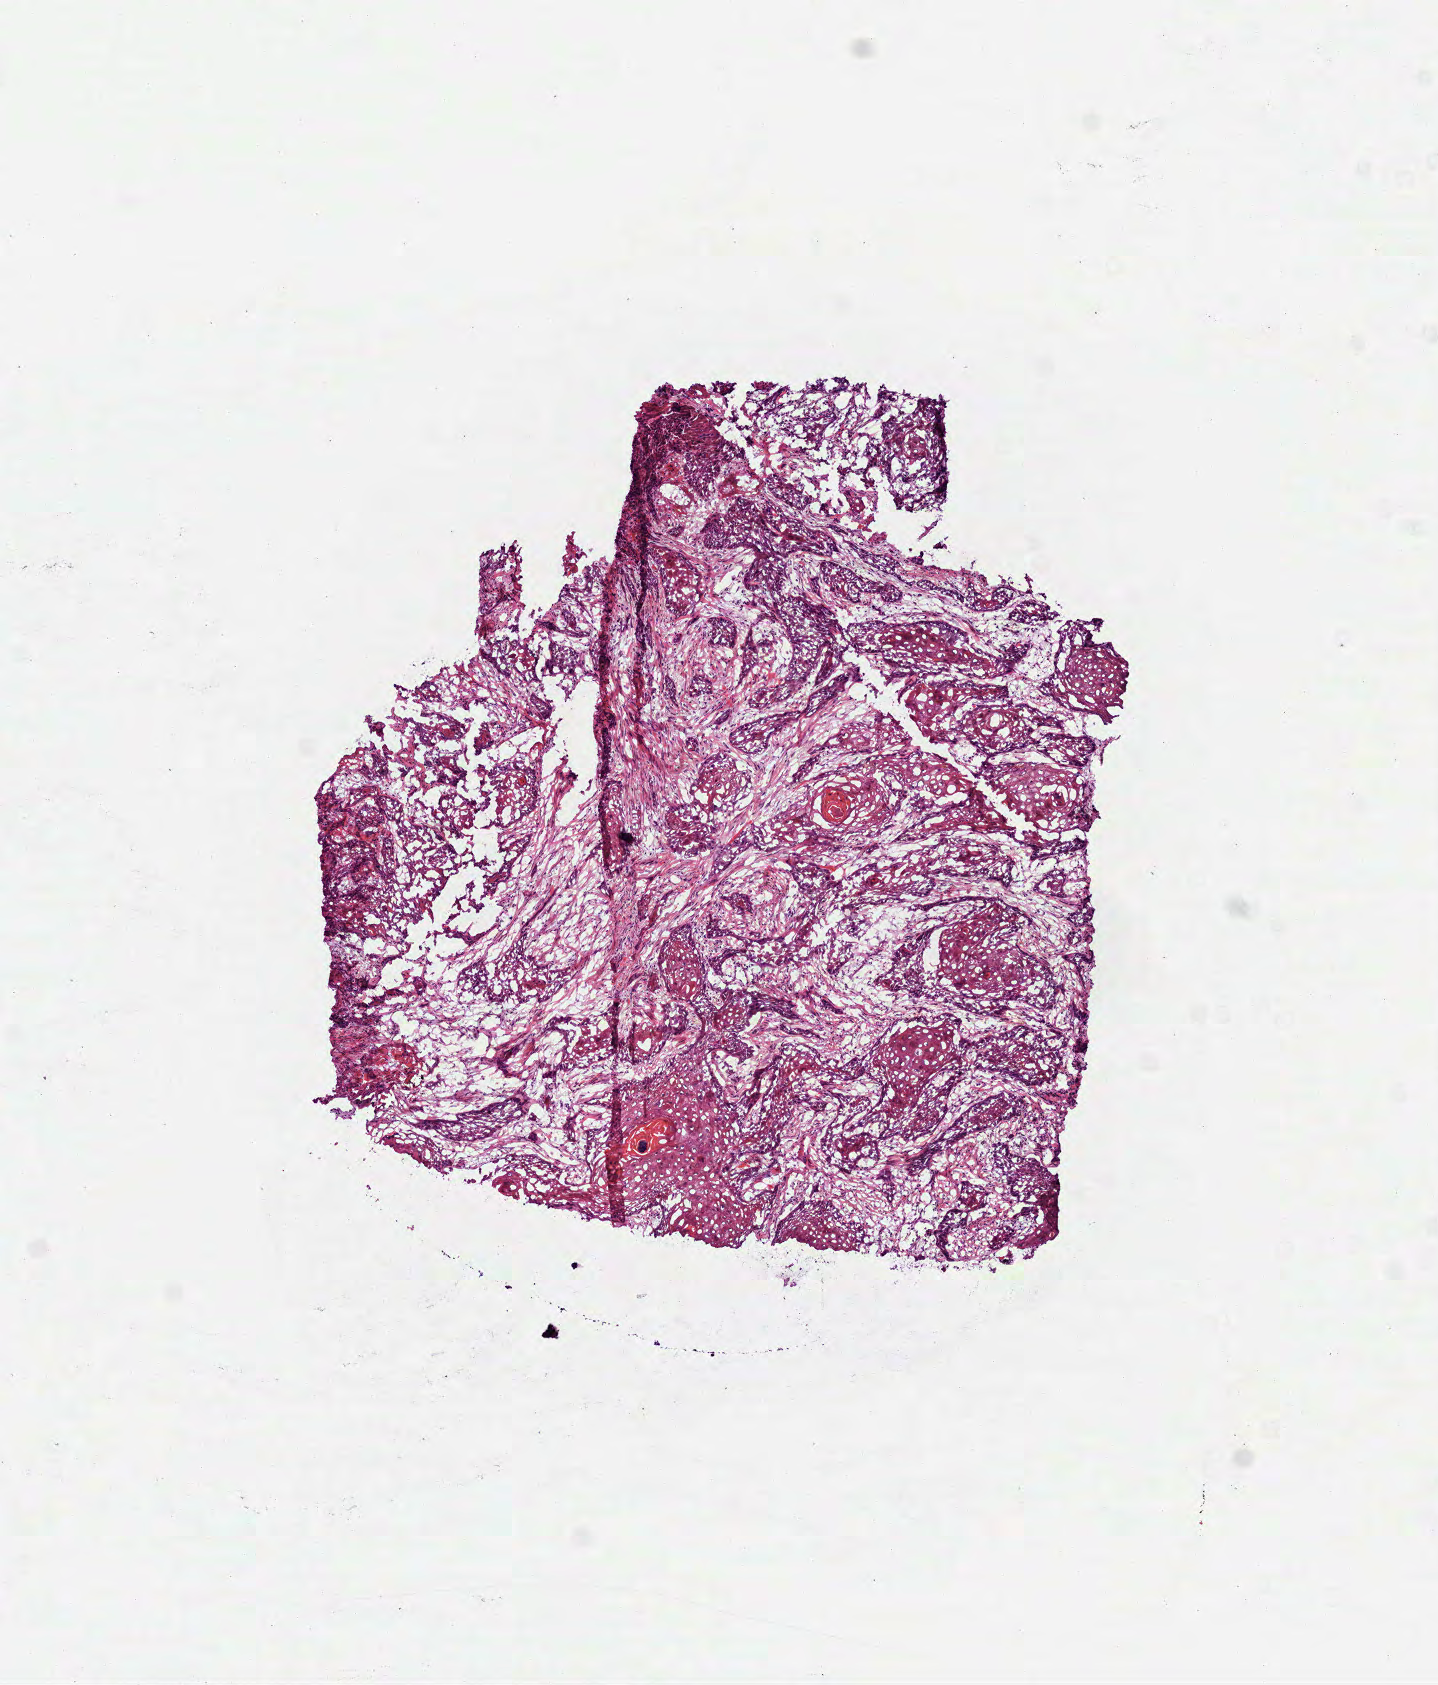
Whole-slide histology image, Hematoxylin and eosin (H&E) stained — shown as a low-resolution overview of the whole scanned area (about 5.8 x 6.8 mm). Frozen section from the top of the tissue portion. Head and neck, primary tumour sample. Patient: male, age at initial diagnosis 41 years. Histologic grade: G2 (moderately differentiated). Composition of this section per pathologist review: tumour cells 99%, tumour nuclei 85%, normal cells 0%, stromal cells 0%, necrosis 1%. Infiltration values recorded for this section: lymphocyte infiltration 1%, monocyte infiltration 0%, neutrophil infiltration 1%.
- TNM: T4a N2
- AJCC pathologic stage: IVA
- diagnosis: Squamous cell carcinoma, NOS (tongue, NOS)